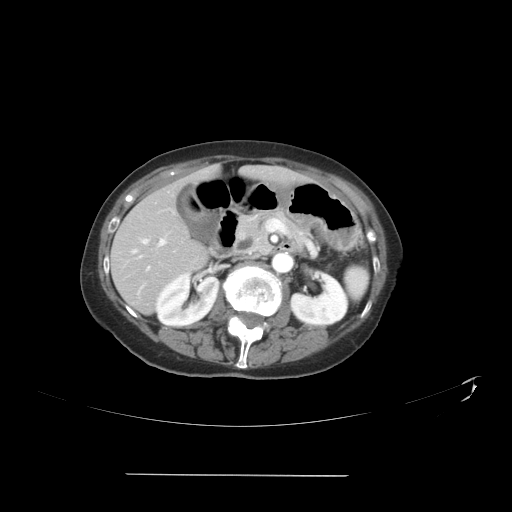
Contrast-enhanced abdominal CT, one axial slice; slice 18 of 41 in the series (ordered by position); reconstruction kernel STANDARD; intravenous contrast given; soft-tissue window (W 400 / L 40 HU); 5 mm slice thickness; 512 × 512 image matrix. Female patient, age 74 years. Case-level facts recorded for this patient, not image findings: diagnosis: colorectal cancer liver metastases, imaged before liver resection; multiple liver metastases: yes; largest metastasis: 3.3 cm; disease in both lobes: yes.
Structures marked on this image (outlined manually by an expert reader):
- hepatic veins: bounding box (x1, y1, x2, y2) in pixels: (132, 239, 150, 271)
- liver: (111, 169, 294, 312)
- planned liver remnant (the part of the liver to remain after resection): (119, 169, 296, 247)
- portal vein (with intrahepatic branches): (139, 239, 165, 258)